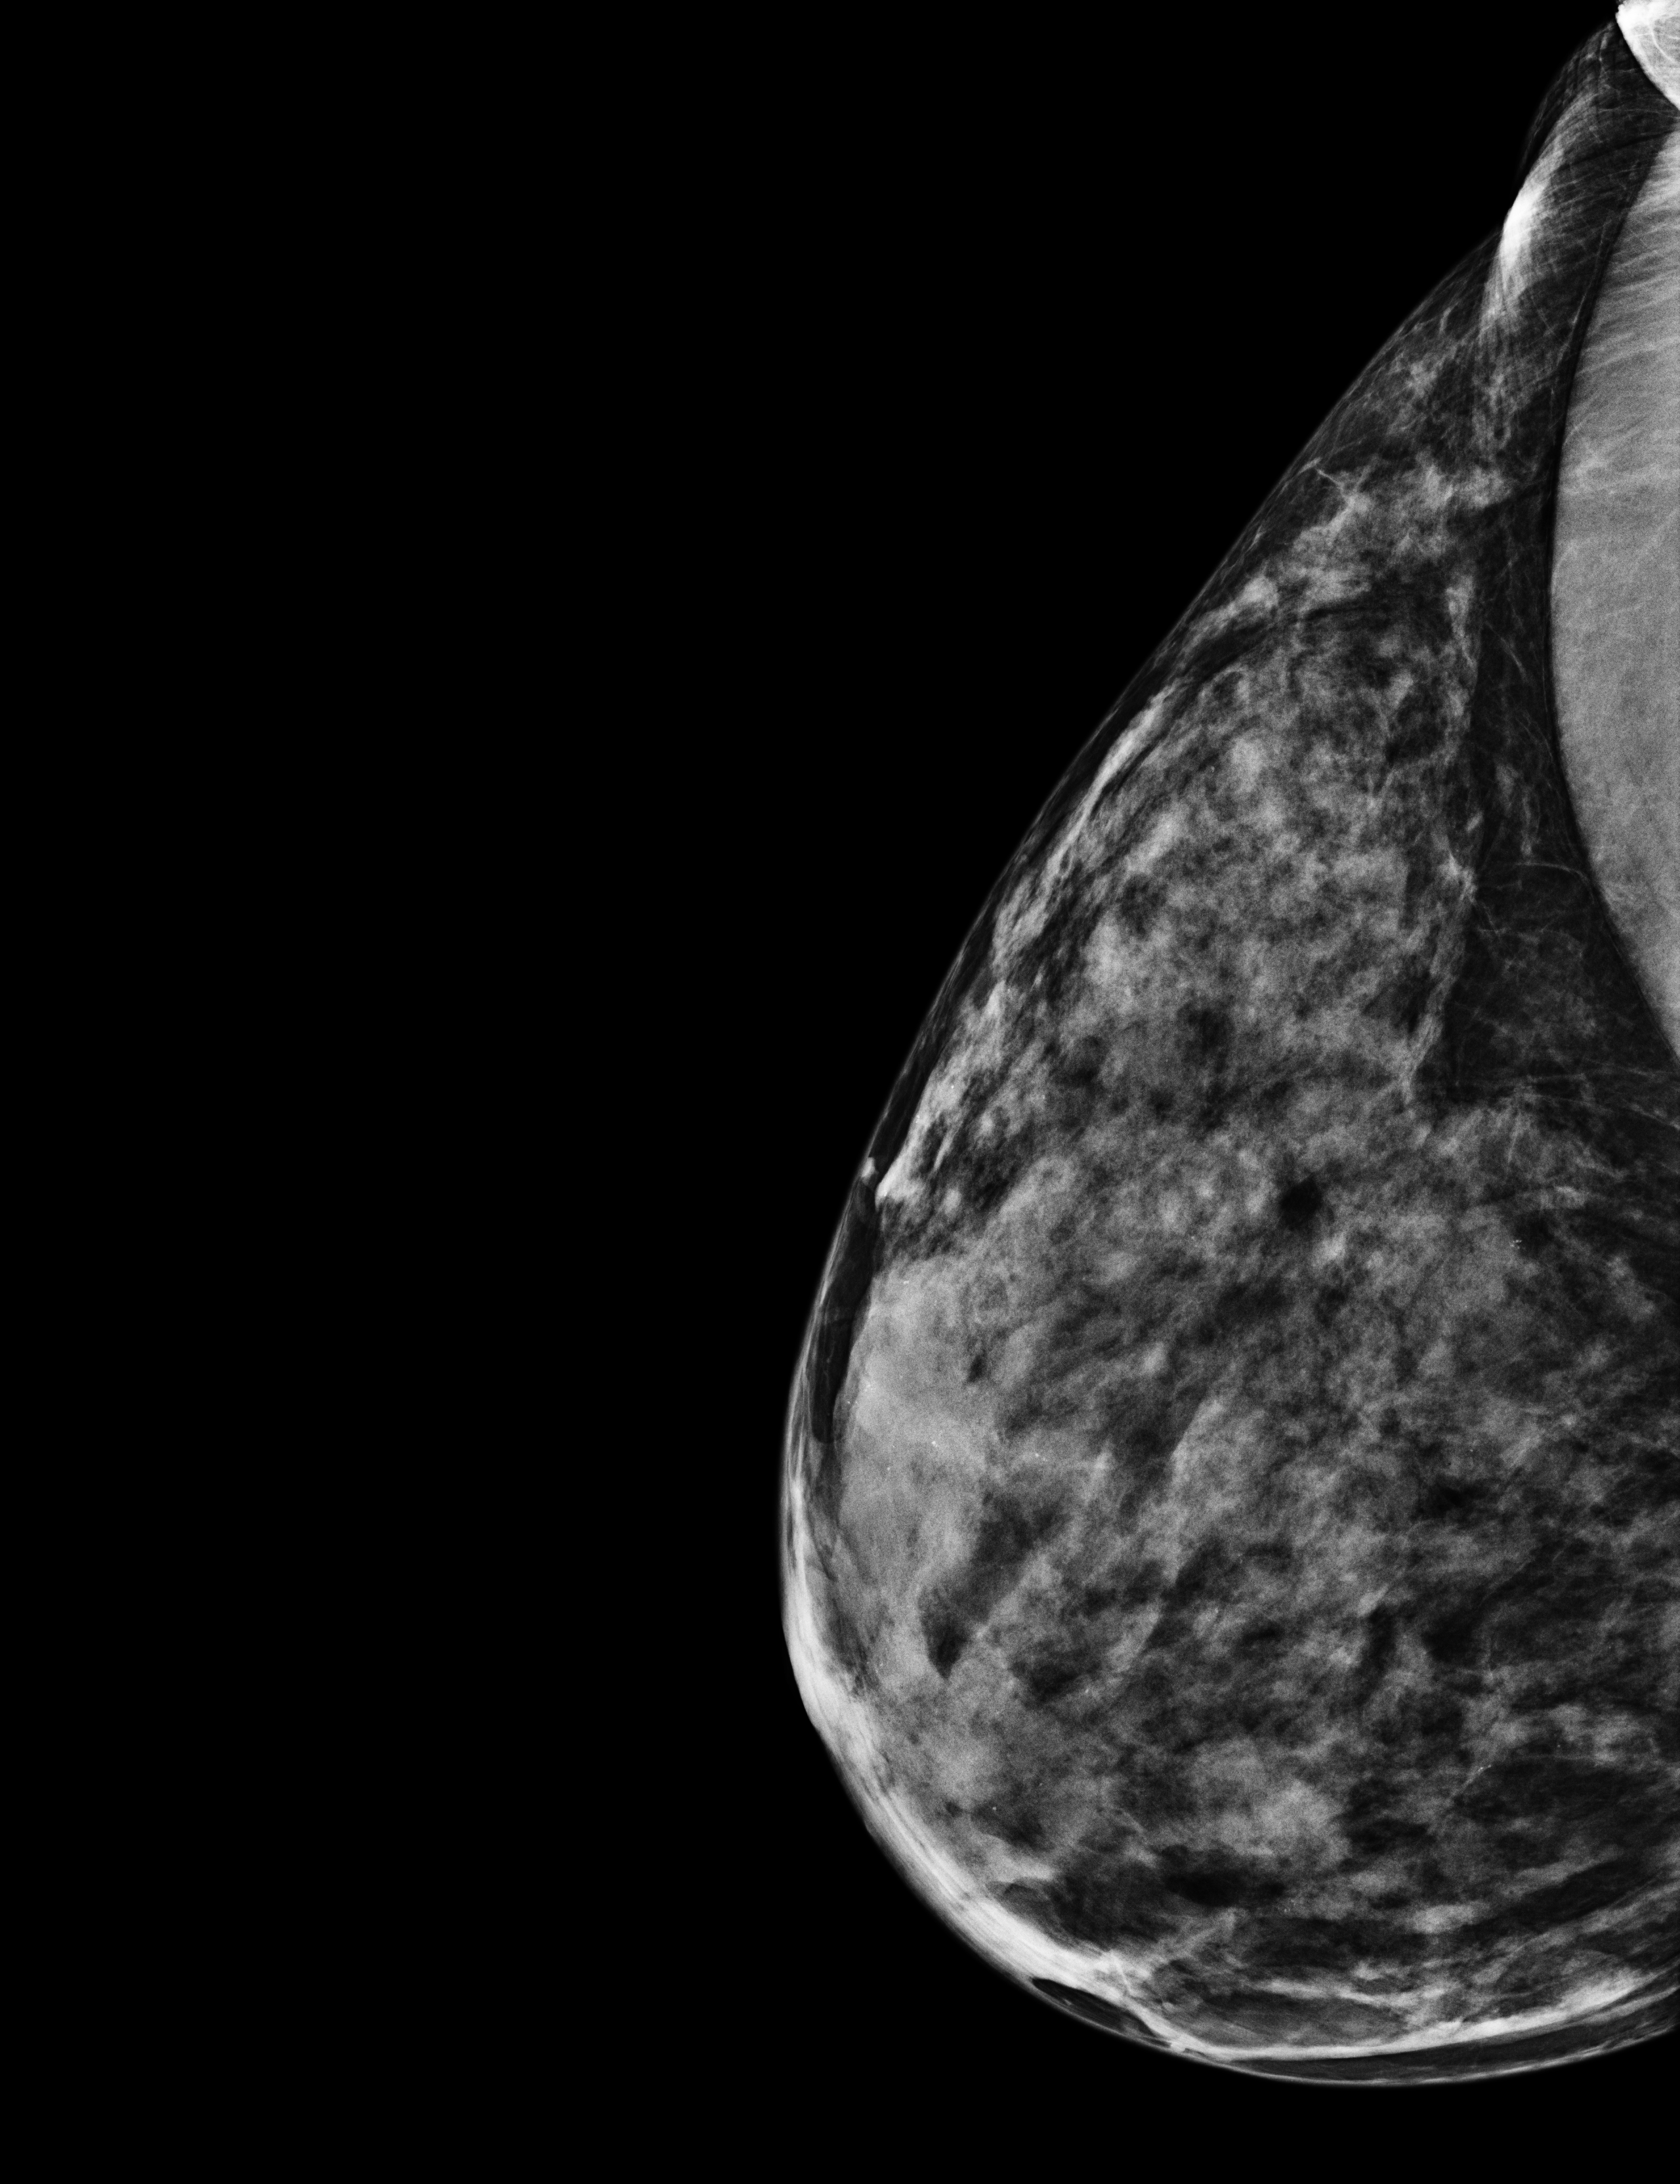
Annual screening mammography examination; system: Selenia Dimensions. Patient: female, 44 years.
Image type: full-field digital mammogram. Breast: right. Projection: exaggerated CC view (lateral).